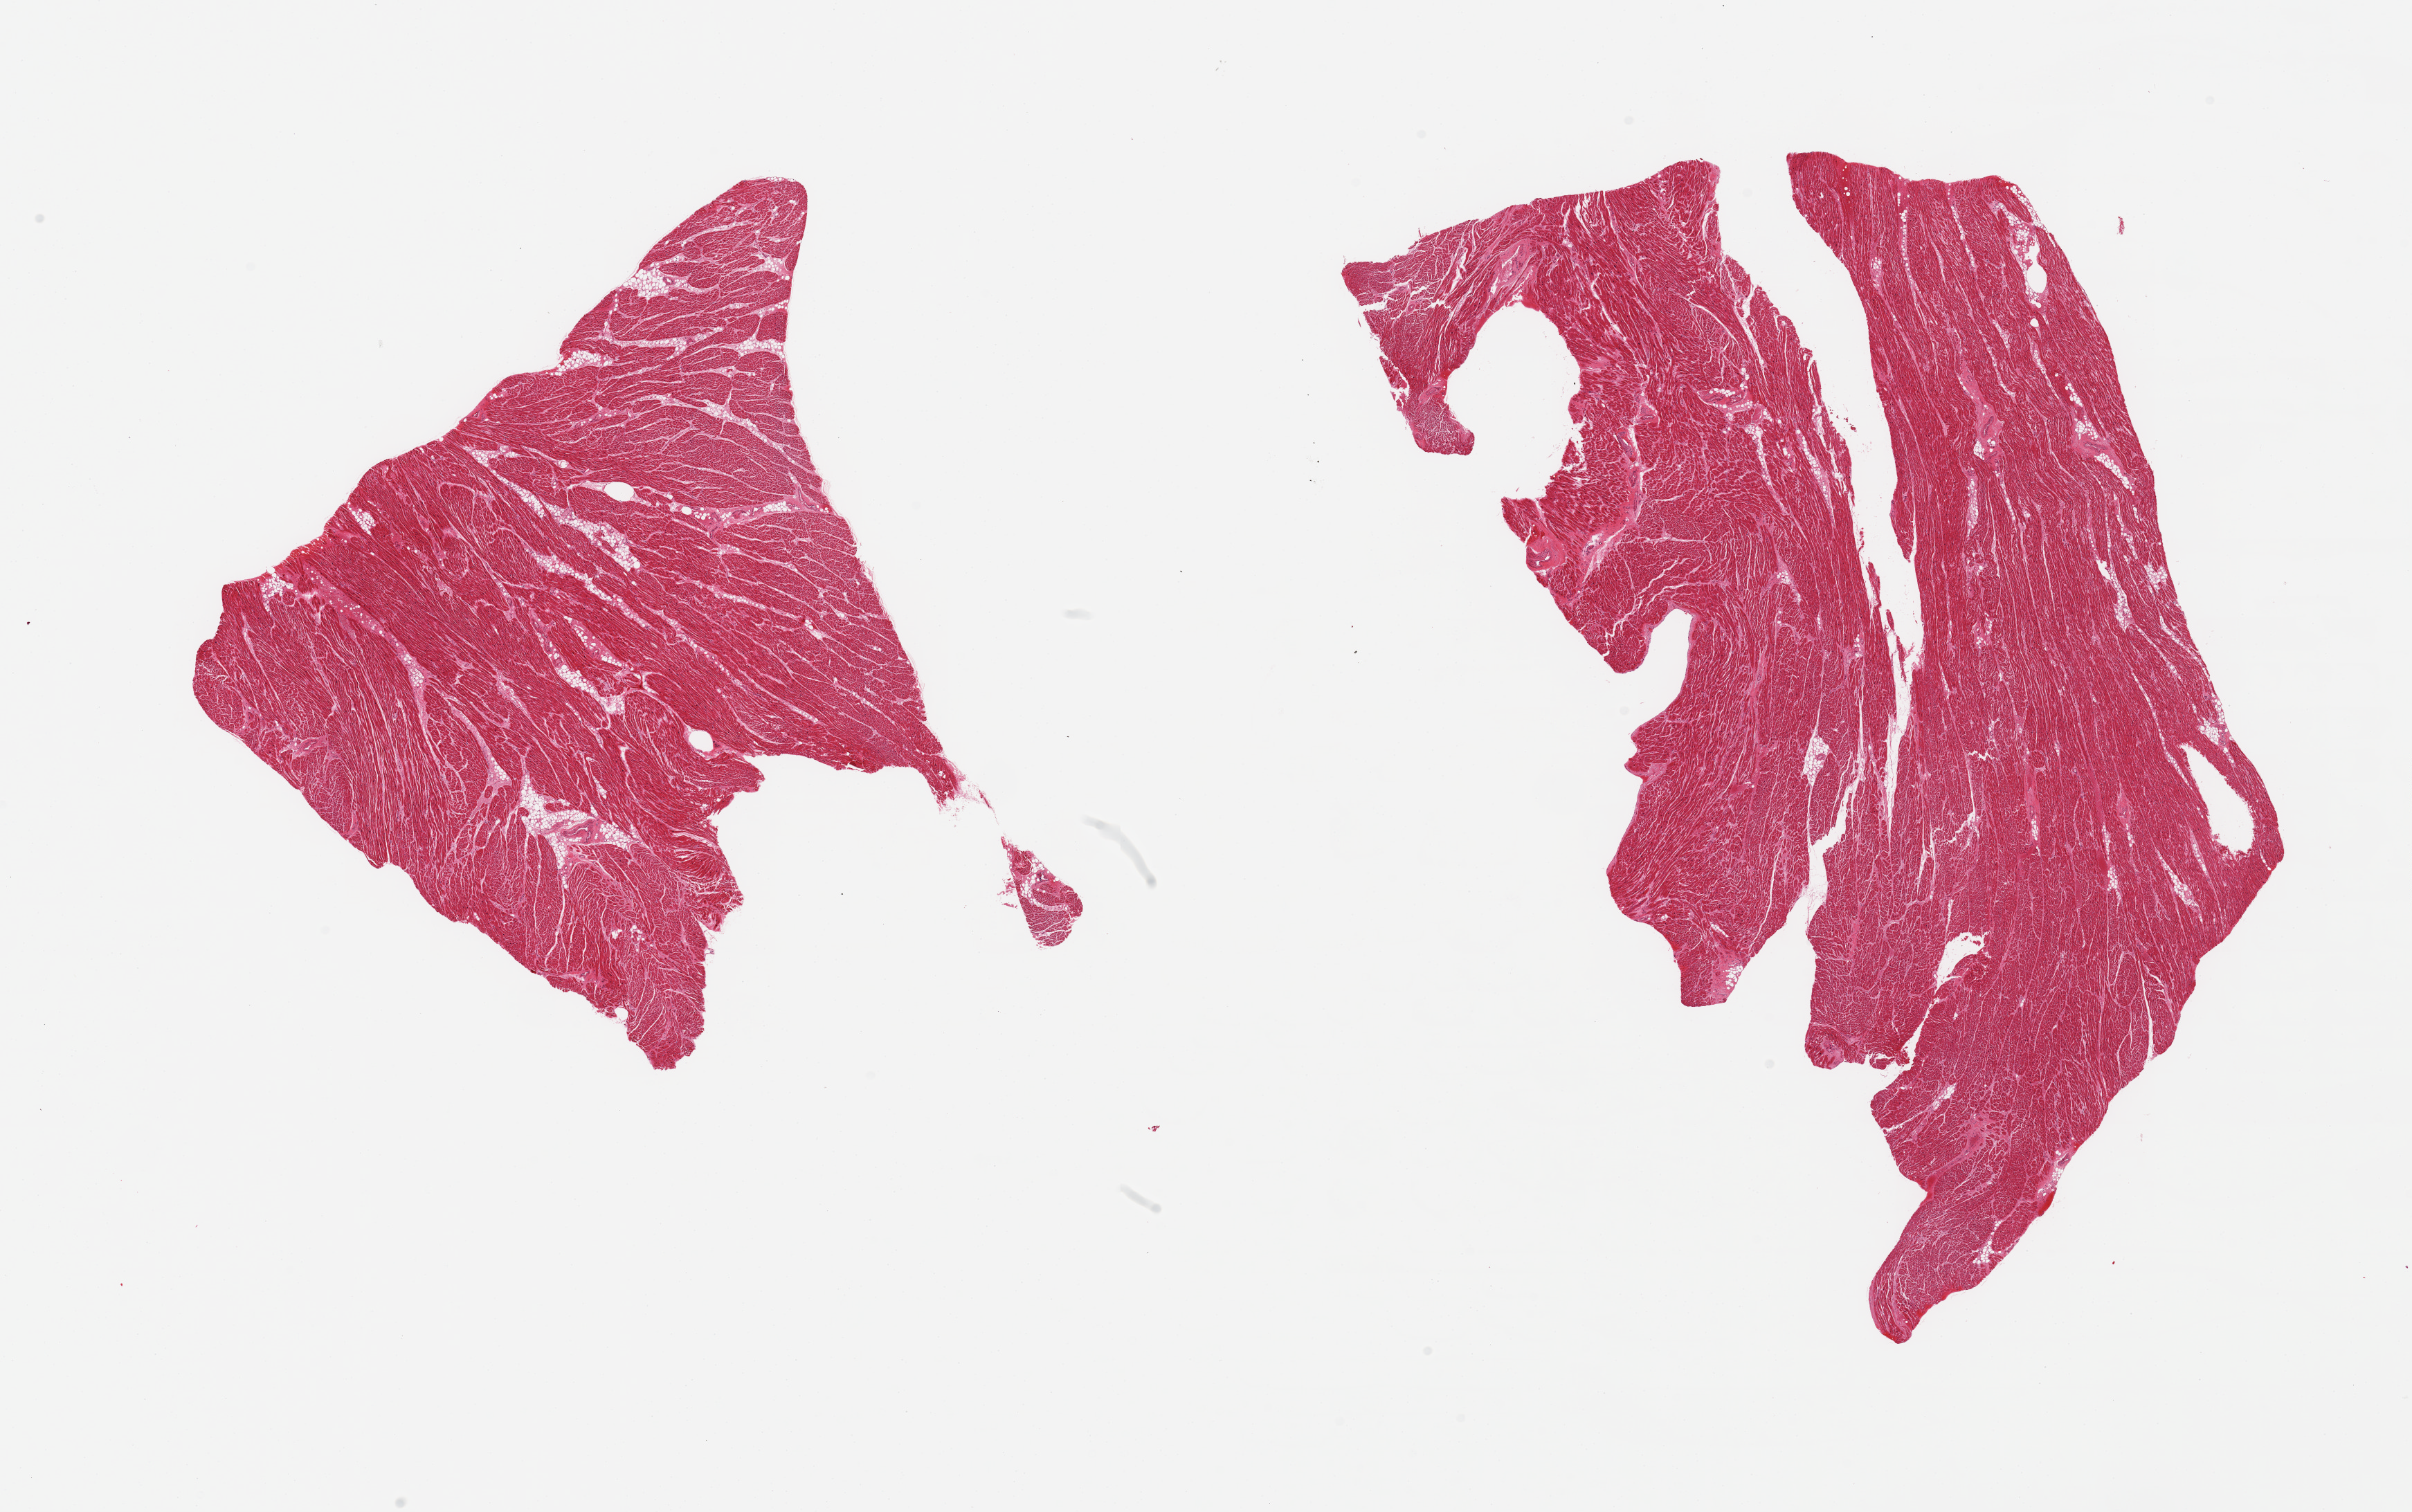
Whole-slide image, H&E stain — shown as a low-resolution overview of the whole scanned area (about 27.6 x 17.3 mm, acquisition: 20x scan). PAXgene-fixed, paraffin-embedded tissue. Section of heart (target tissue). Donor tissue sample. Donor sex: male.
Pathologist's review note for this sample: 2 pieces; small amount of internal fat, some boxcar nuclei suggesting myocyte hypertrophy, focal influx of neutrophils.